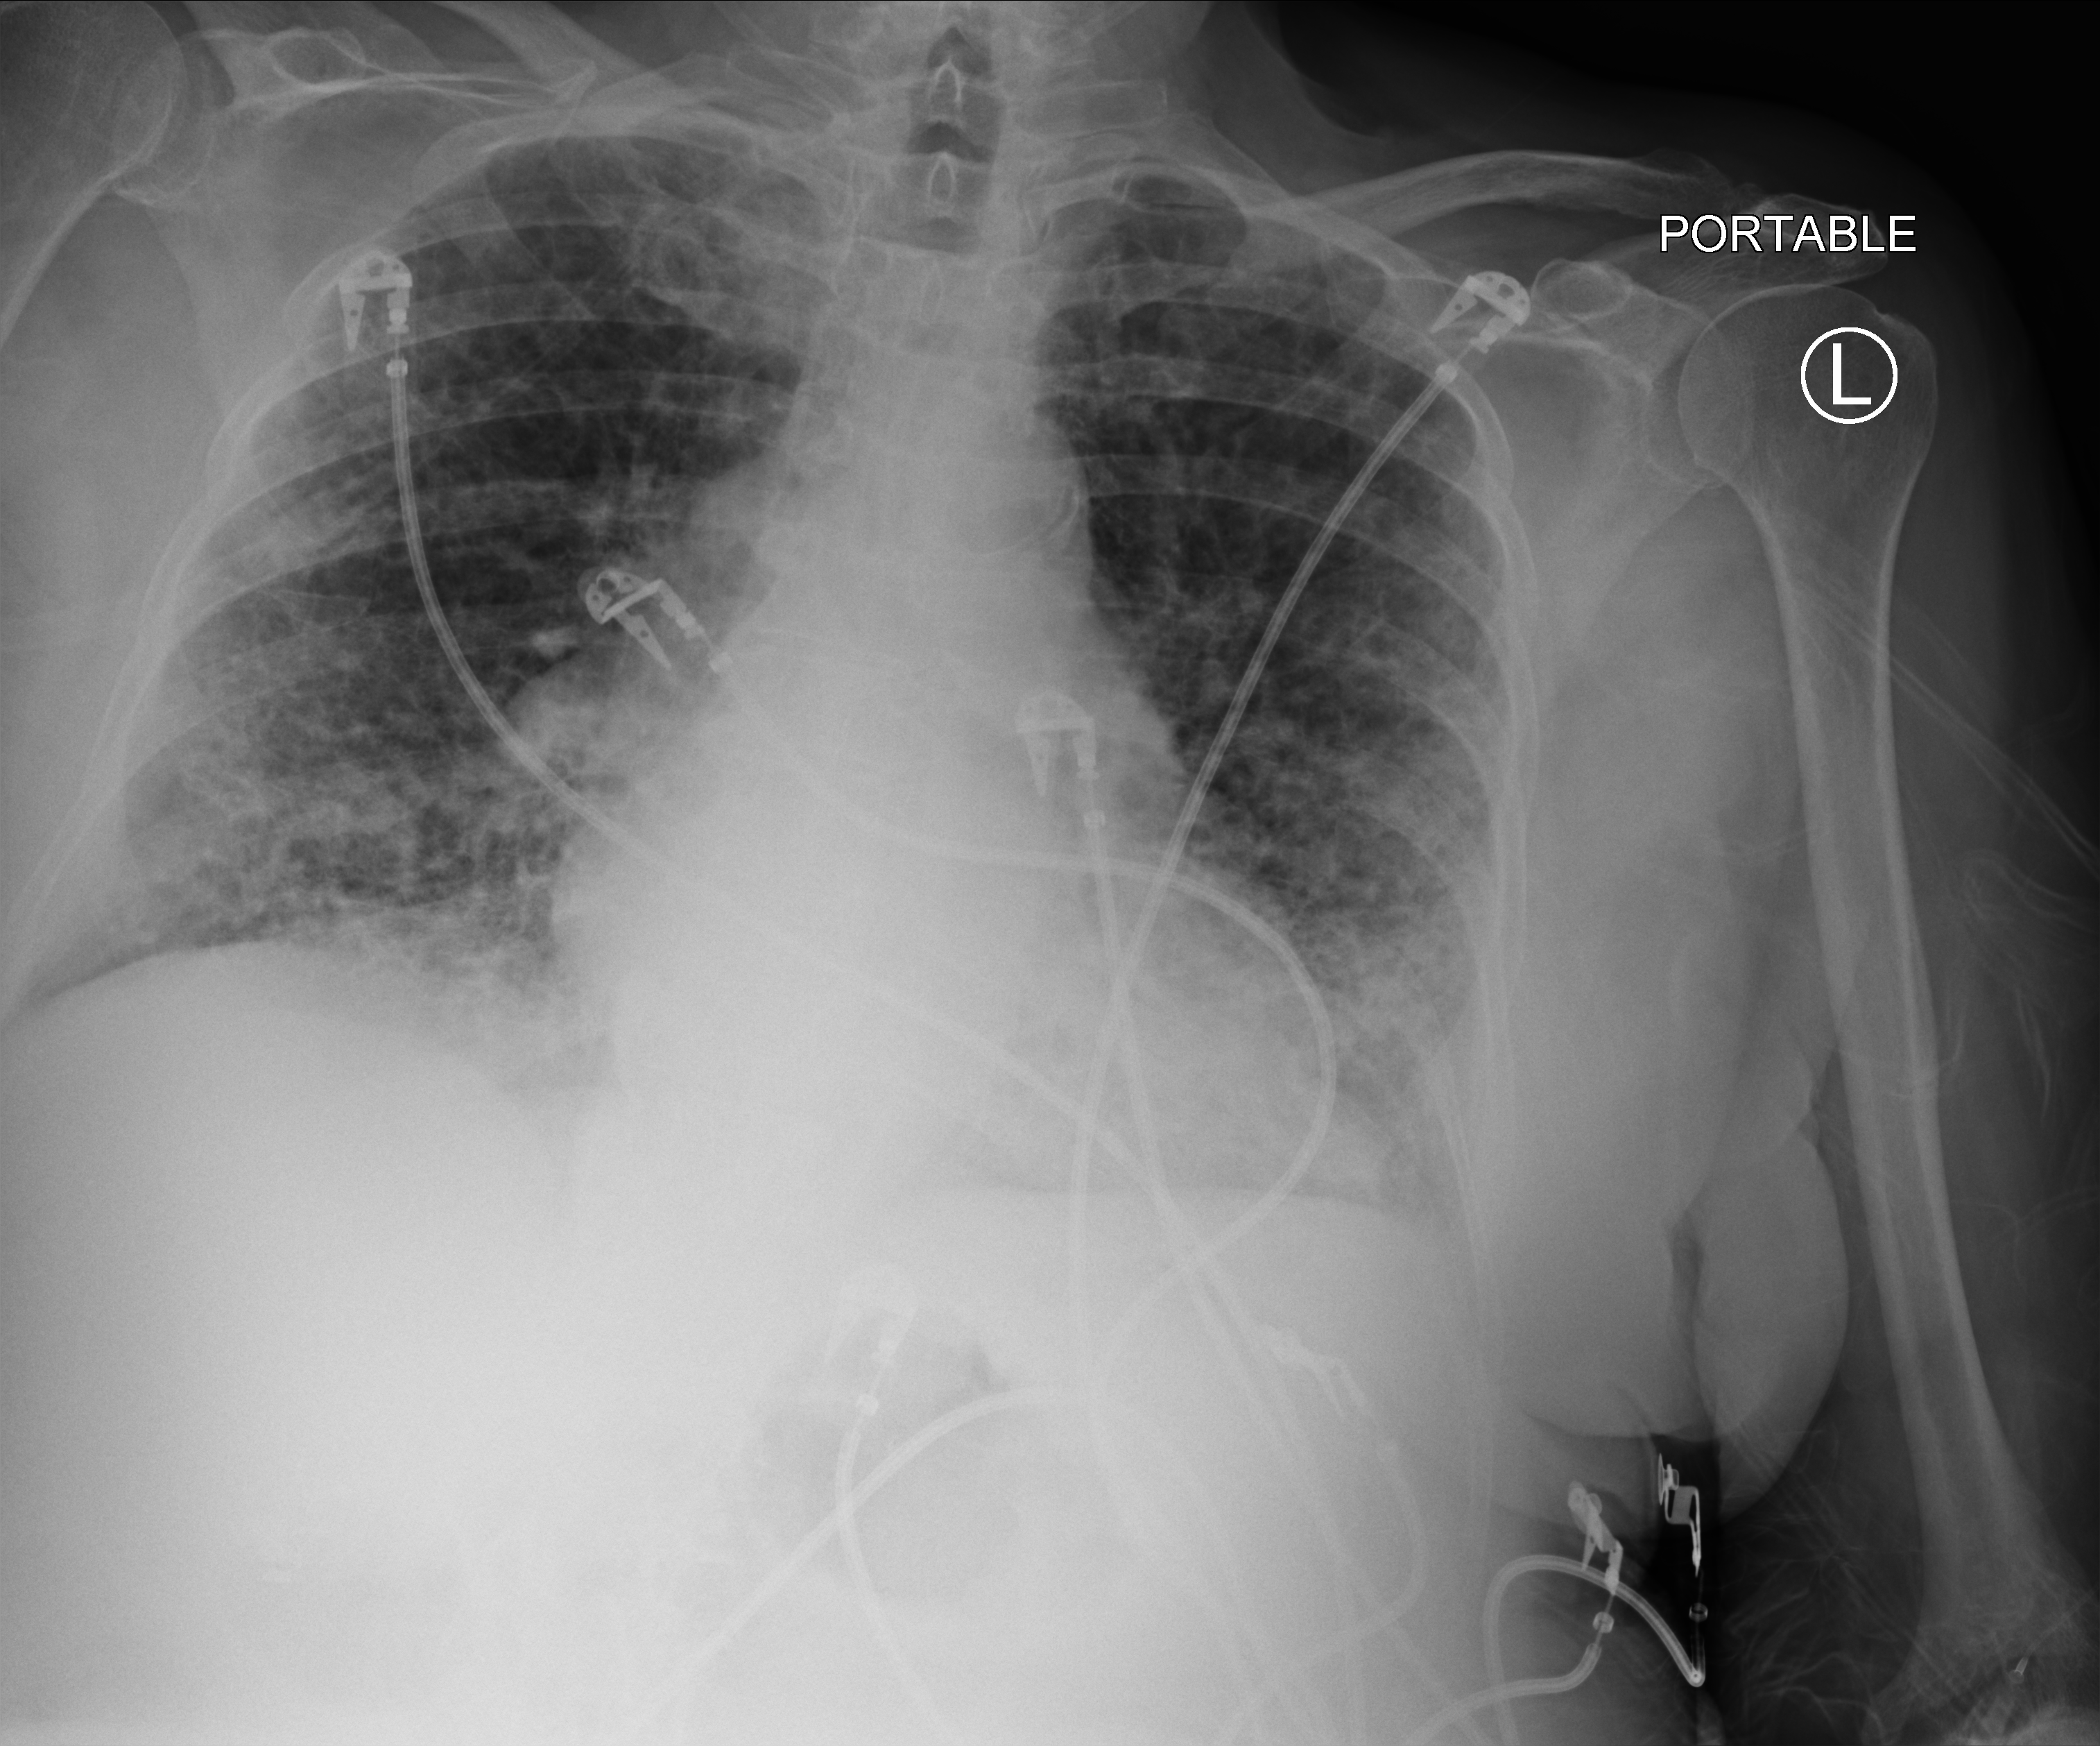
Bedside chest radiograph (computed radiography), anteroposterior (AP) projection. Female patient hospitalised with COVID-19, age 75–90 years.
Admission-level facts for this patient (not findings on this image; timing relative to this image not recorded): admitted to intensive care during this hospital stay: no; length of hospital stay: 19 days; chronic kidney disease (admission record): no.